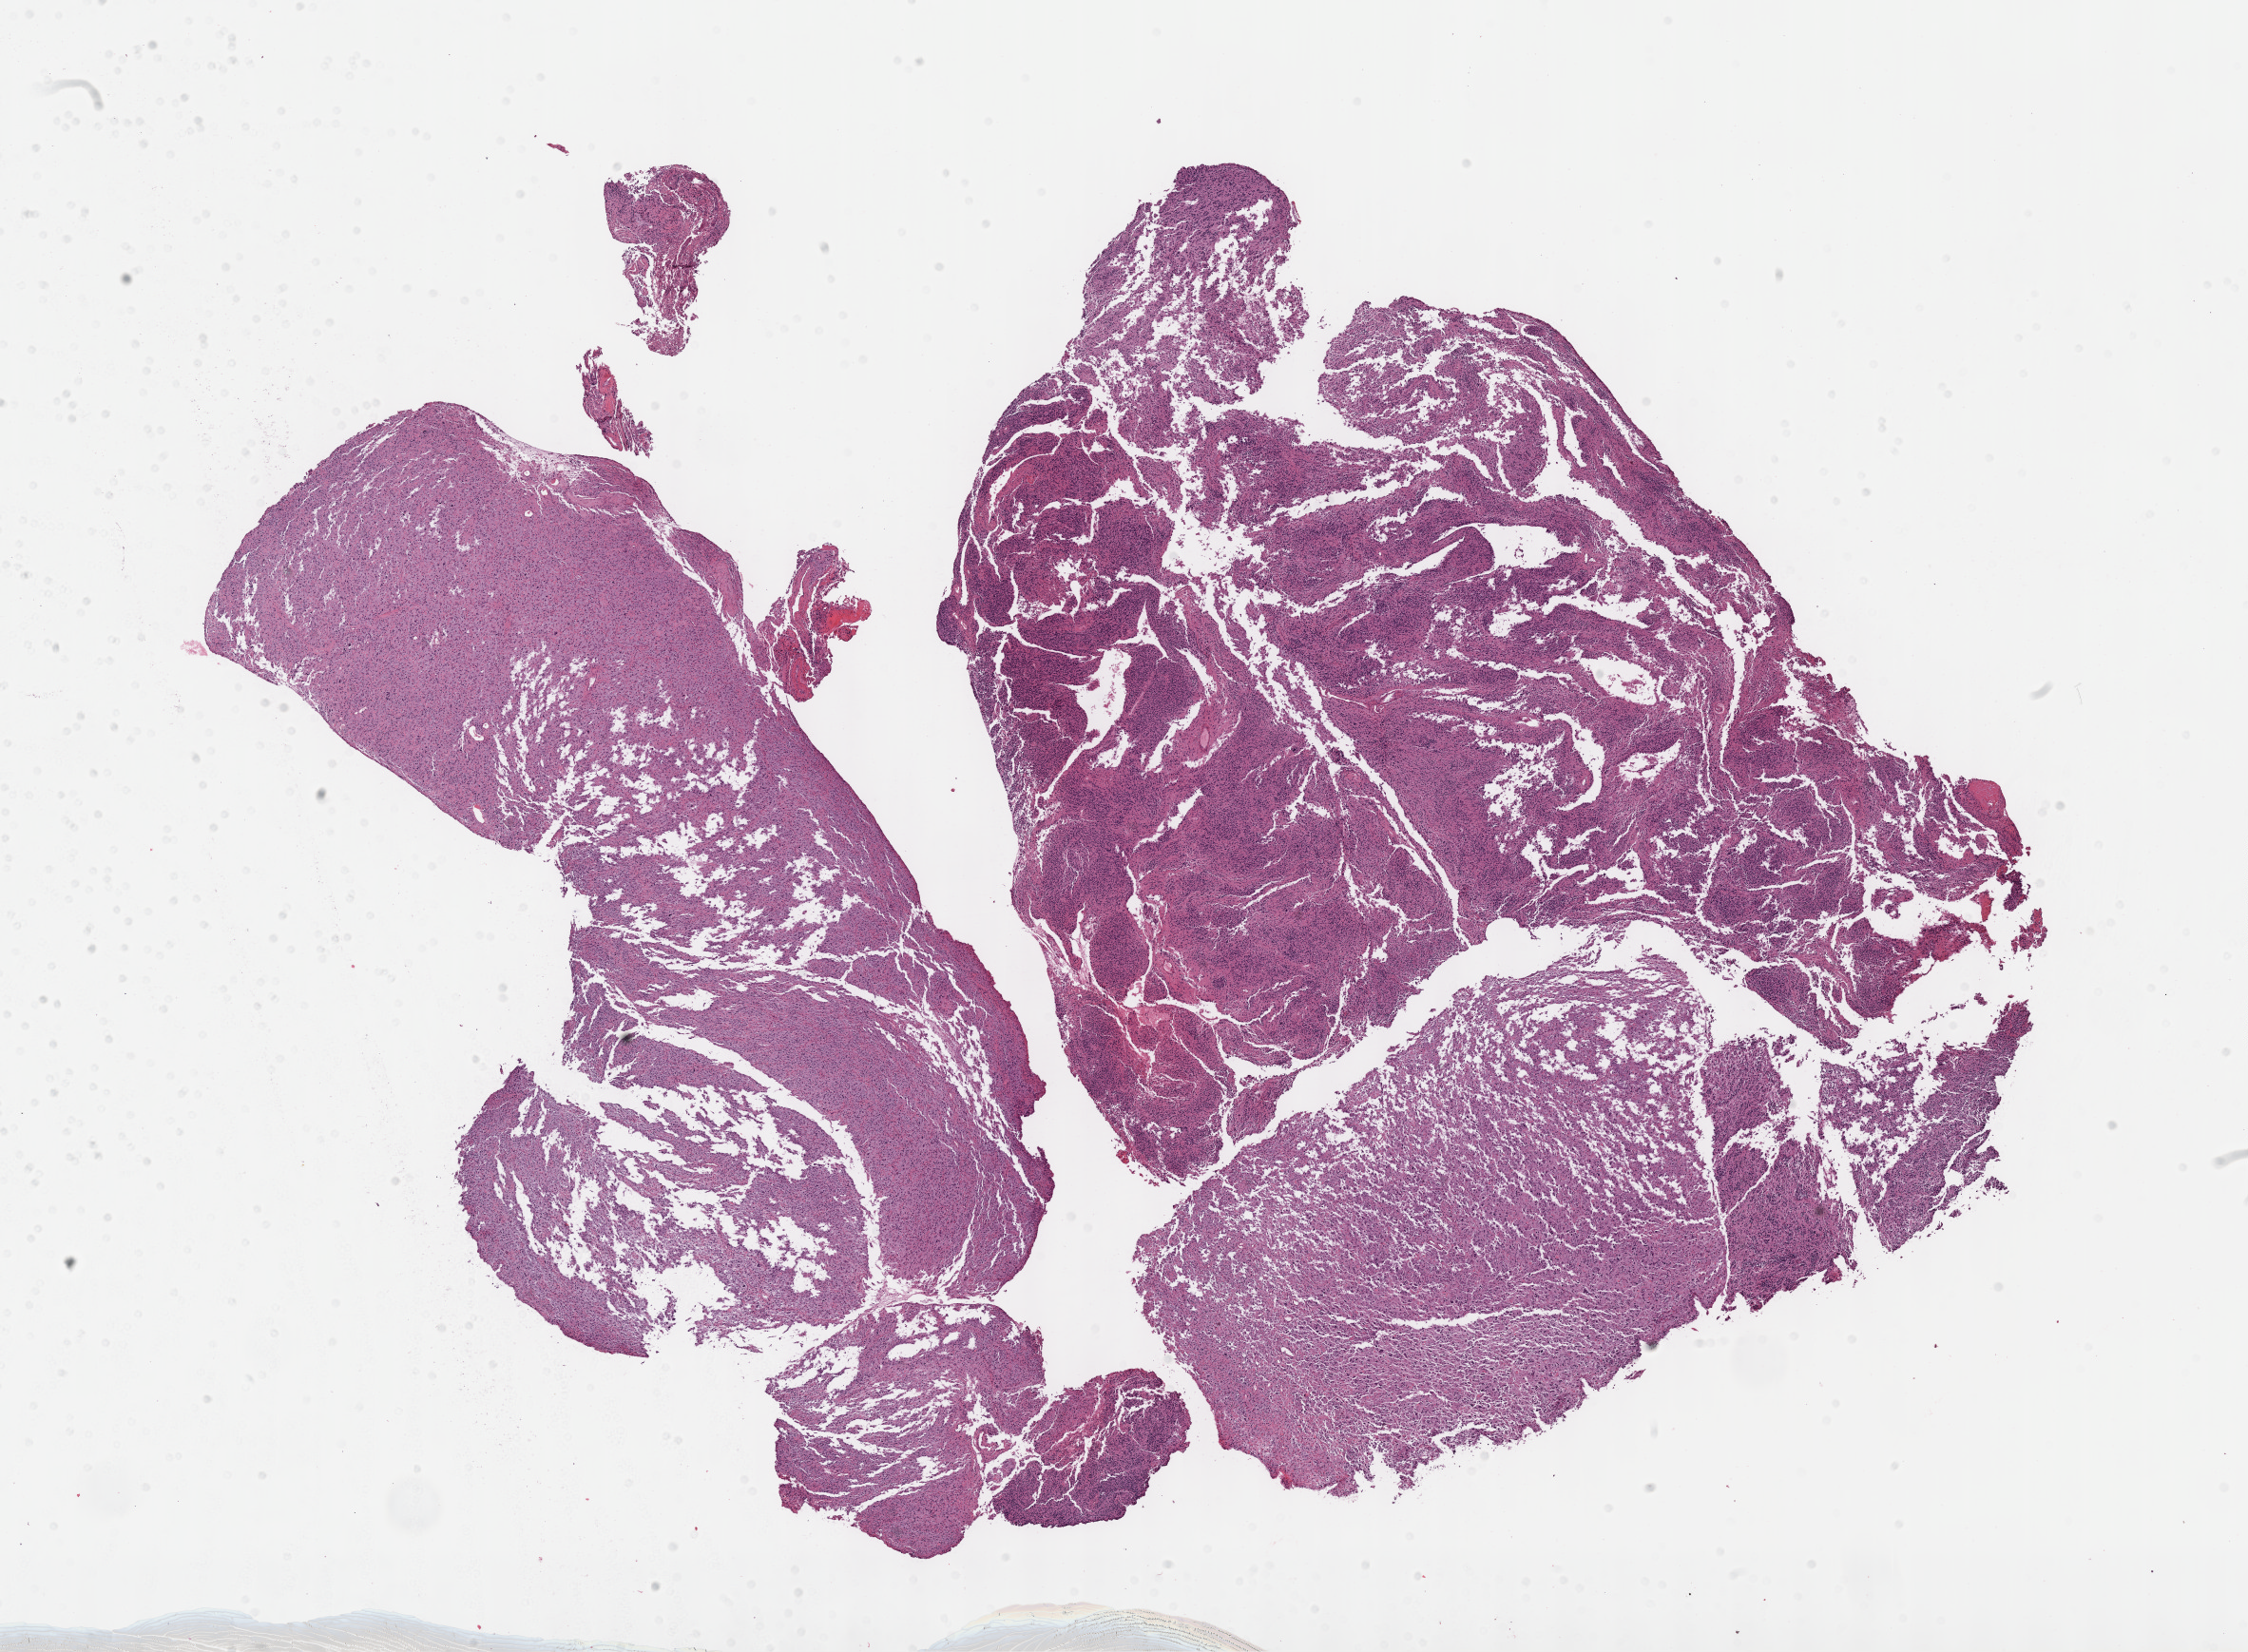
Hematoxylin and eosin (H&E) stained whole-slide image, a low-resolution overview of the entire scanned area, about 19.1 x 14.1 mm (from a 40x scan). FFPE section. Brain, primary tumour sample. Male patient; age at initial diagnosis 29 years. Histologic grade: G3 (poorly differentiated).
Pathologic diagnosis: Mixed glioma. Laterality: right.